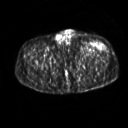
FDG PET of an extremity soft-tissue mass (from a PET/CT study), one axial slice. Position 258 of 267 along the scan axis. 128 × 128 image matrix. Male patient, age 64 years. From the clinical record (not read from this slice): histological type: extraskeletal osteosarcoma; grade: high; site of the primary tumour: thigh.
Outlined on this slice (expert contour drawn on MRI and transferred to this co-registered scan by the dataset authors):
- gross tumour volume (mass): box from (x=93, y=42) to (x=105, y=49) px